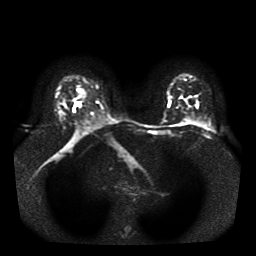
Breast MRI, one axial slice. Slice 28 of 41 in the series (ordered by position). Diffusion-weighted series; image 2 of 4 stored at this slice position (different b-values; order by instance number). 1.5 T. 5 mm slice thickness. 256 × 256 image matrix, field of view 330 × 330 mm. Female patient.
Structures marked on this image (manually delineated by an expert):
- tumour on diffusion-weighted imaging: bounding box (x1, y1, x2, y2) in pixels: (72, 102, 82, 112)